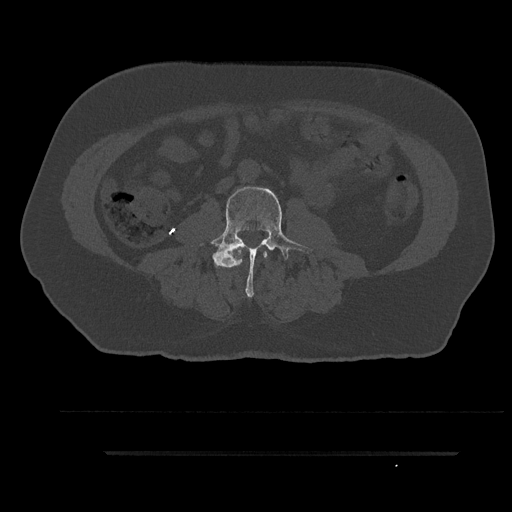
CT including the spine, one axial slice; slice 43 of 797 in the series (ordered by position); bone window (W 1800 / L 400 HU); 0.5 mm slice thickness; 512 × 512 image matrix. Patient: male, 63 years. From the clinical record (not read from this slice): primary cancer: renal.
Annotated regions visible in this slice (semi-automatic segmentation, software-assisted and operator-edited):
- L2 vertebra: bounding box <235,249,268,266> (left, top, right, bottom; pixels)
- L3 vertebra: <199,185,313,297>